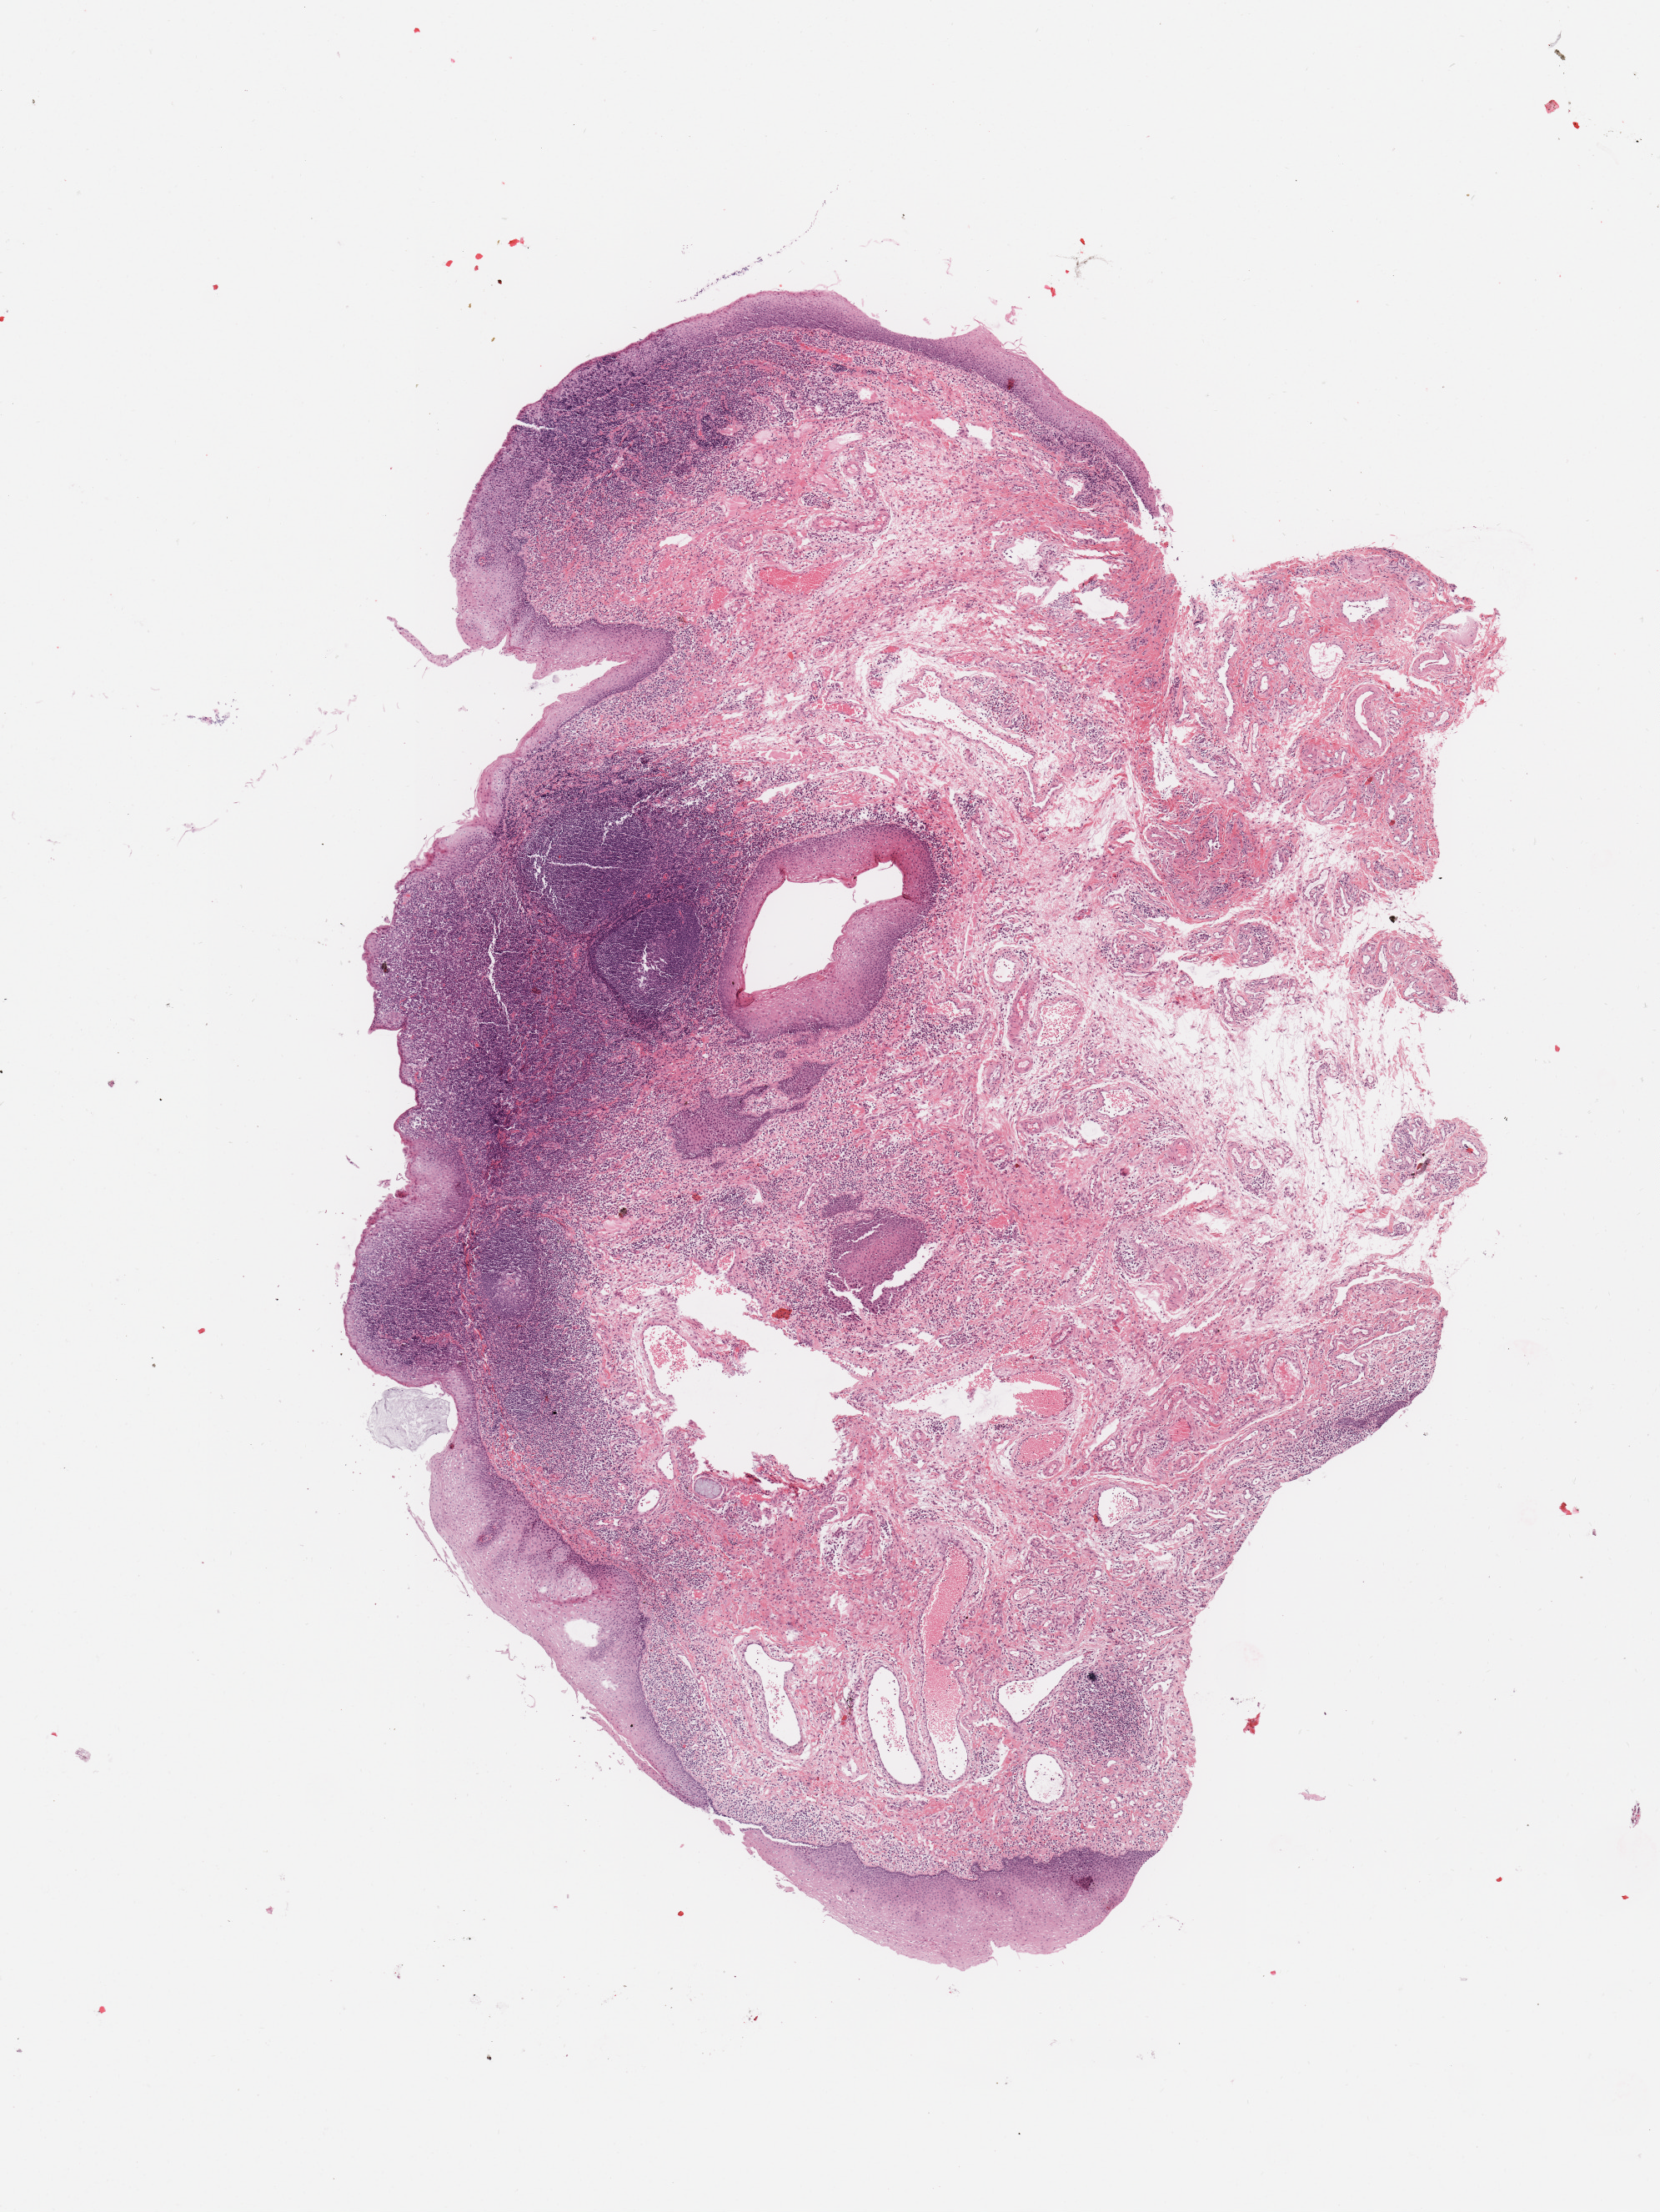
H&E whole-slide image, low-resolution overview of the scanned area, about 7.9 x 10.5 mm (acquisition: 20x scan); normal (non-tumour) tissue sample, sampled site: larynx. 65-year-old male patient.
This section: normal (non-tumour) tissue from the same patient. Patient diagnosis: Squamous cell carcinoma, NOS (larynx, NOS).